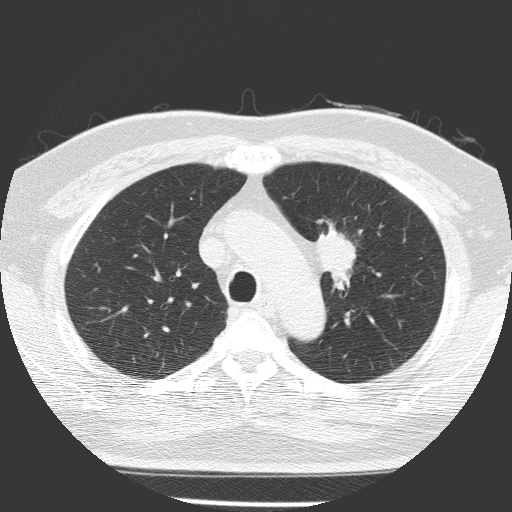
Axial slice from a low-dose chest CT screening exam, baseline screening round, lung window (W 1500 / L -600 HU), 2 mm slice thickness, lung (sharp) reconstruction kernel (FC51). Male participant, aged 70 years at enrolment. Current smoker at enrolment.
Expert reader's lesion annotation, bounding box (x1, y1, x2, y2) in pixels: (298, 223, 371, 297). The screening reader recorded 3 non-calcified nodules or masses ≥4 mm on this exam (left upper lobe, left lower lobe, left upper lobe); which of them this box marks is not recorded.